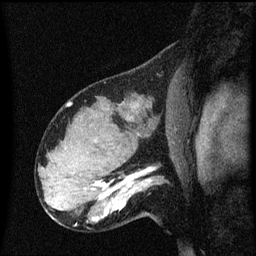
Breast MRI (dynamic contrast-enhanced), one sagittal slice. Dynamic contrast-enhanced series, image 2 of 3 at this slice position (ordered by acquisition). 1.5 T. TE 4.2 ms, TR 8.4 ms. 2 mm slice thickness. 256 × 256 image matrix, field of view 200 × 200 mm. Patient: female, 31 years. Case-level facts recorded for this patient, not image findings: setting: breast cancer imaged before/during neoadjuvant chemotherapy; receptor status: HR-positive, HER2-negative.
Outlined on this slice (semi-automatically segmented with operator editing):
- analysis volume of interest (the breast-tissue region the enhancement analysis was run in; not a lesion): bounding box [x1, y1, x2, y2] px = [102, 166, 168, 221]
- tumour enhancement mask (voxels above the 70 % enhancement threshold inside the analysis volume of interest): [102, 168, 155, 217]